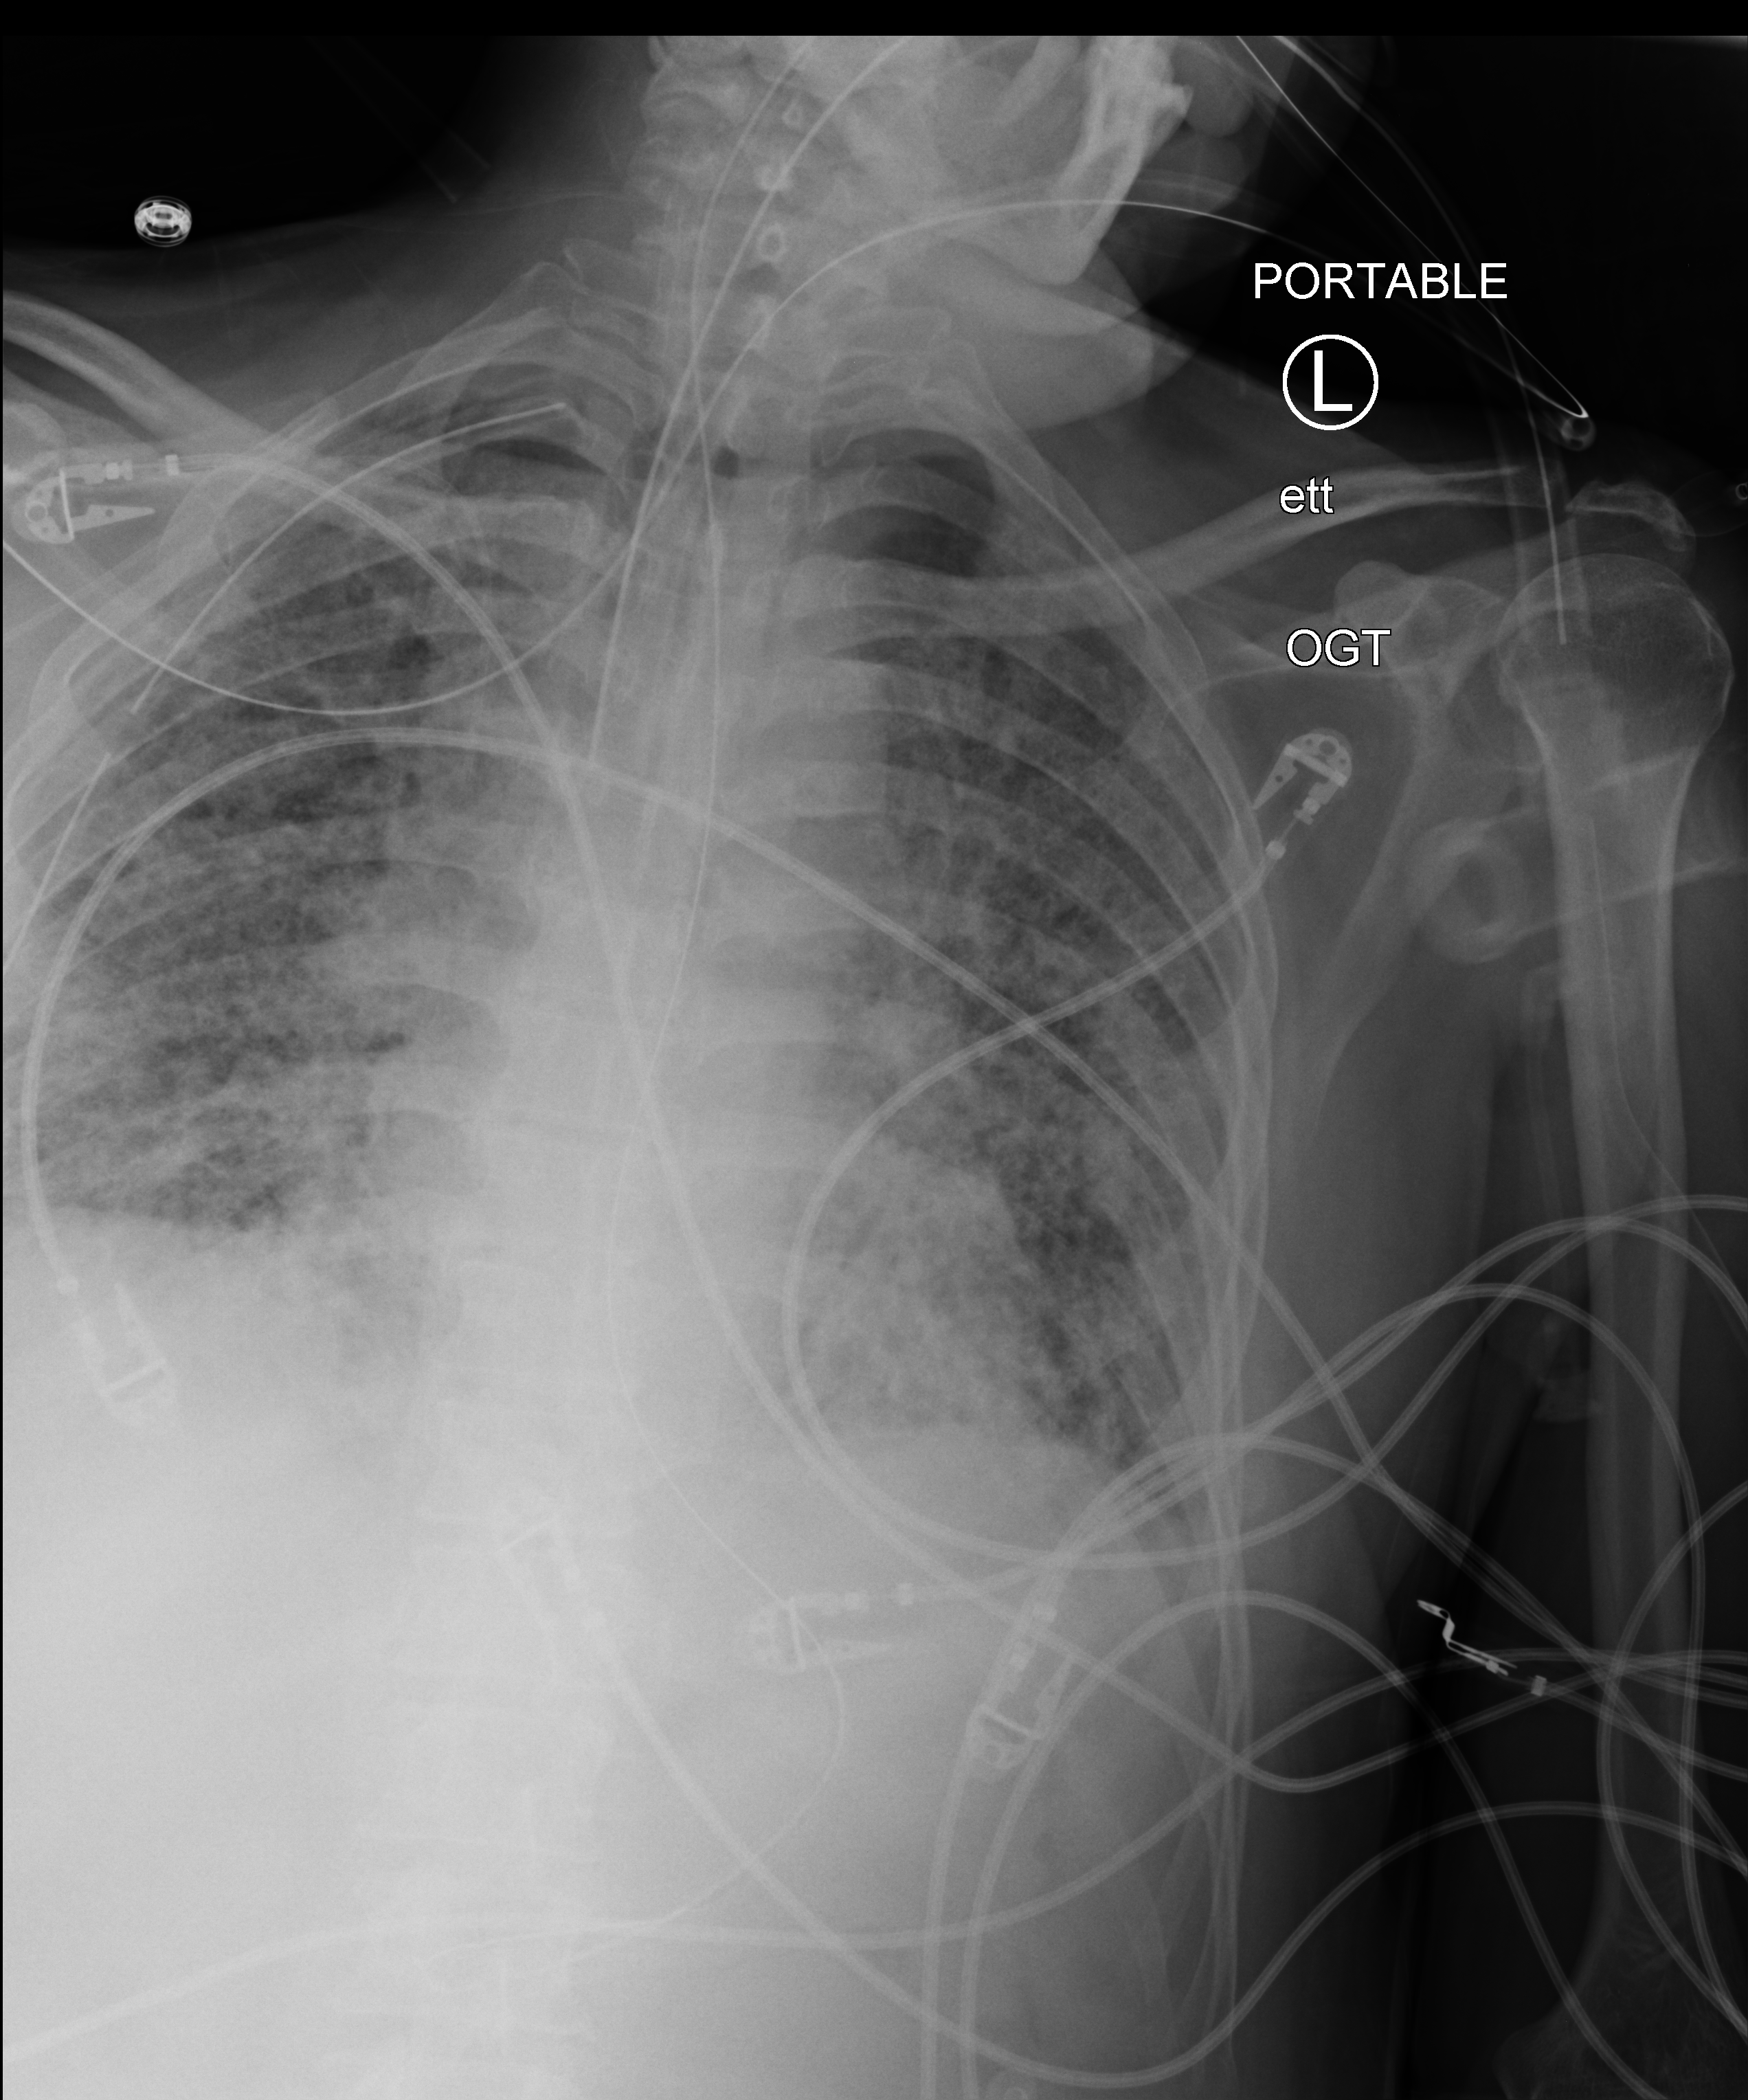
Portable chest radiograph, anteroposterior (AP) projection. Patient hospitalised with COVID-19; male, aged 60–74 years.
Hospital-stay facts (about this admission, not read from this image; timing relative to this image not recorded): mechanically ventilated during this hospital stay: yes.